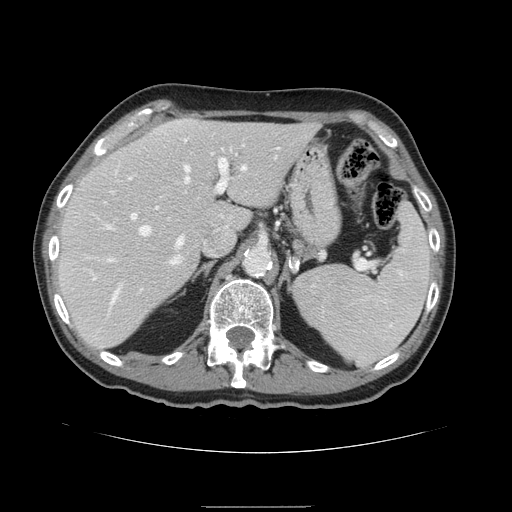
Contrast-enhanced abdominal CT, one axial slice; position 103 of 168 along the scan axis; intravenous contrast given; soft-tissue window (W 400 / L 40 HU); 512 × 512 image matrix, field of view 386 × 386 mm. Male patient, age 74 years. Case-level facts recorded for this patient, not image findings: diagnosis: colorectal cancer liver metastases, imaged before liver resection; multiple liver metastases: no.
Annotated regions visible in this slice (manually delineated by an expert):
- hepatic veins: bounding box (x1, y1, x2, y2) in pixels: (108, 165, 246, 302)
- liver: (57, 118, 320, 349)
- planned liver remnant (the part of the liver to remain after resection): (56, 118, 320, 349)
- portal vein (with intrahepatic branches): (102, 158, 228, 247)